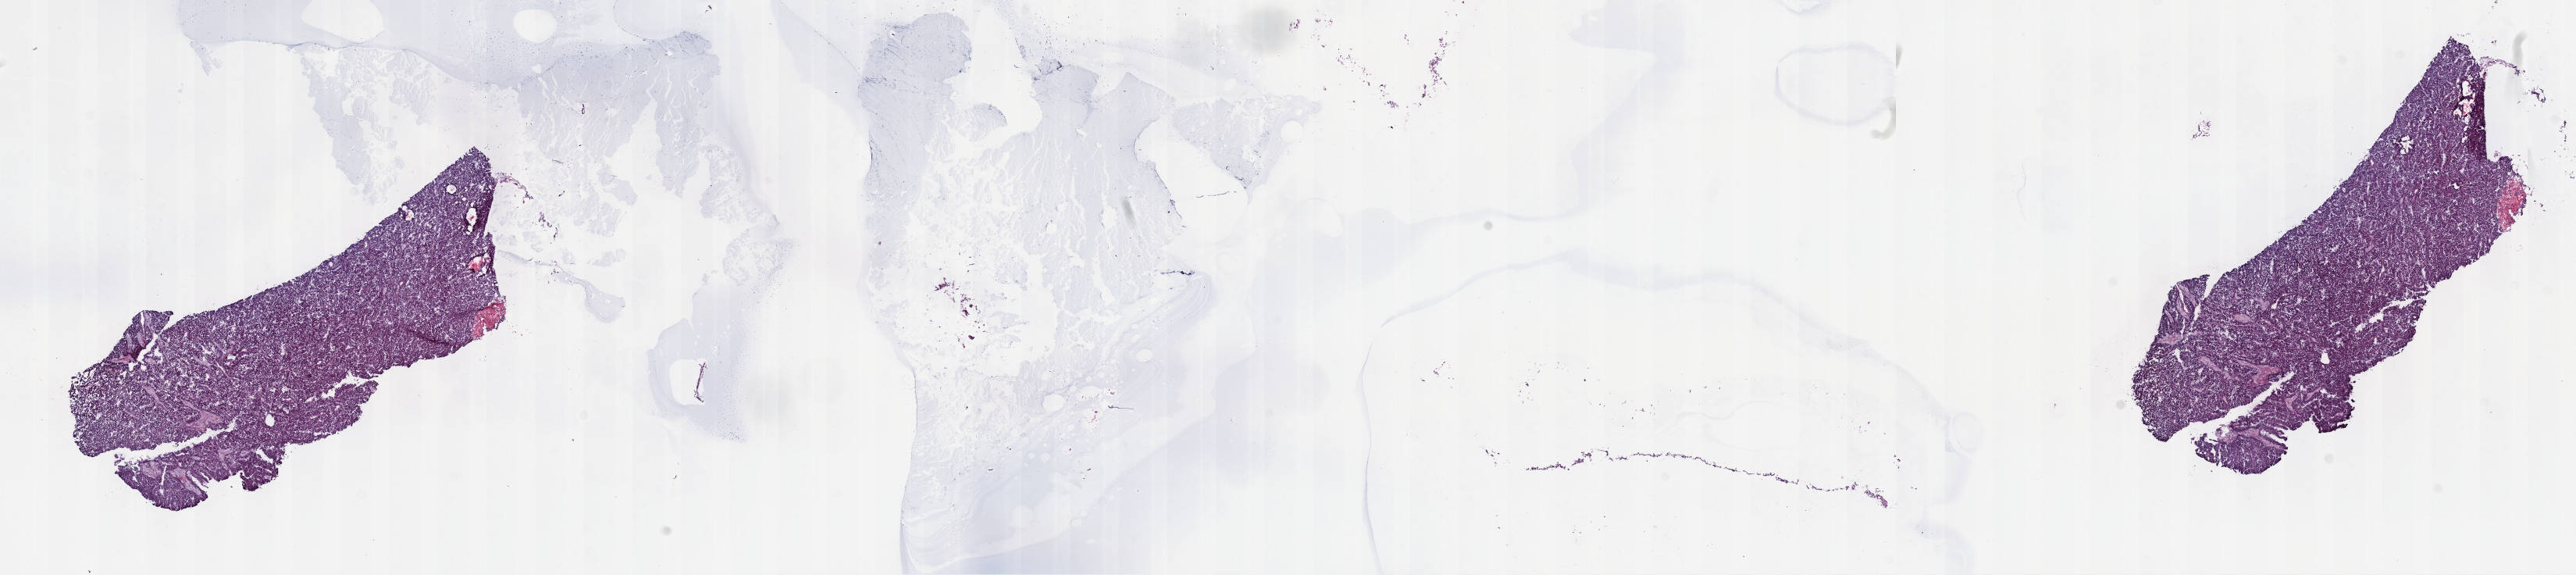
Whole-slide histology image, H&E, whole scanned area (about 26.7 x 6.0 mm, acquisition: 40x scan) shown as a low-resolution overview; frozen section from the top of the tissue portion; primary tumour sample from the kidney. Female, age 71 years at initial diagnosis. Pathologist review of this section (percent, as recorded): tumour cells 90%, tumour nuclei 92%, normal cells 1%, stromal cells 7%, necrosis 2%. Infiltration values recorded for this section: lymphocyte infiltration 3%, monocyte infiltration 4%, neutrophil infiltration 0%.
Pathologic diagnosis: Papillary adenocarcinoma, NOS. AJCC pathologic stage: I.